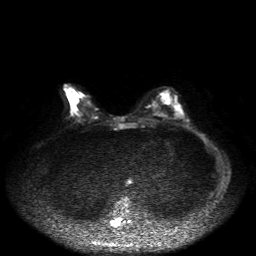
Breast MRI, one axial slice; position 19 of 50 along the scan axis; diffusion-weighted series; image 2 of 4 stored at this slice position (different b-values; order by instance number); 1.5 T; 256 × 256 image matrix, field of view 360 × 360 mm. Female patient.
Outlined on this slice (expert manual segmentation):
- tumour on diffusion-weighted imaging: box from (x=73, y=100) to (x=77, y=103) px